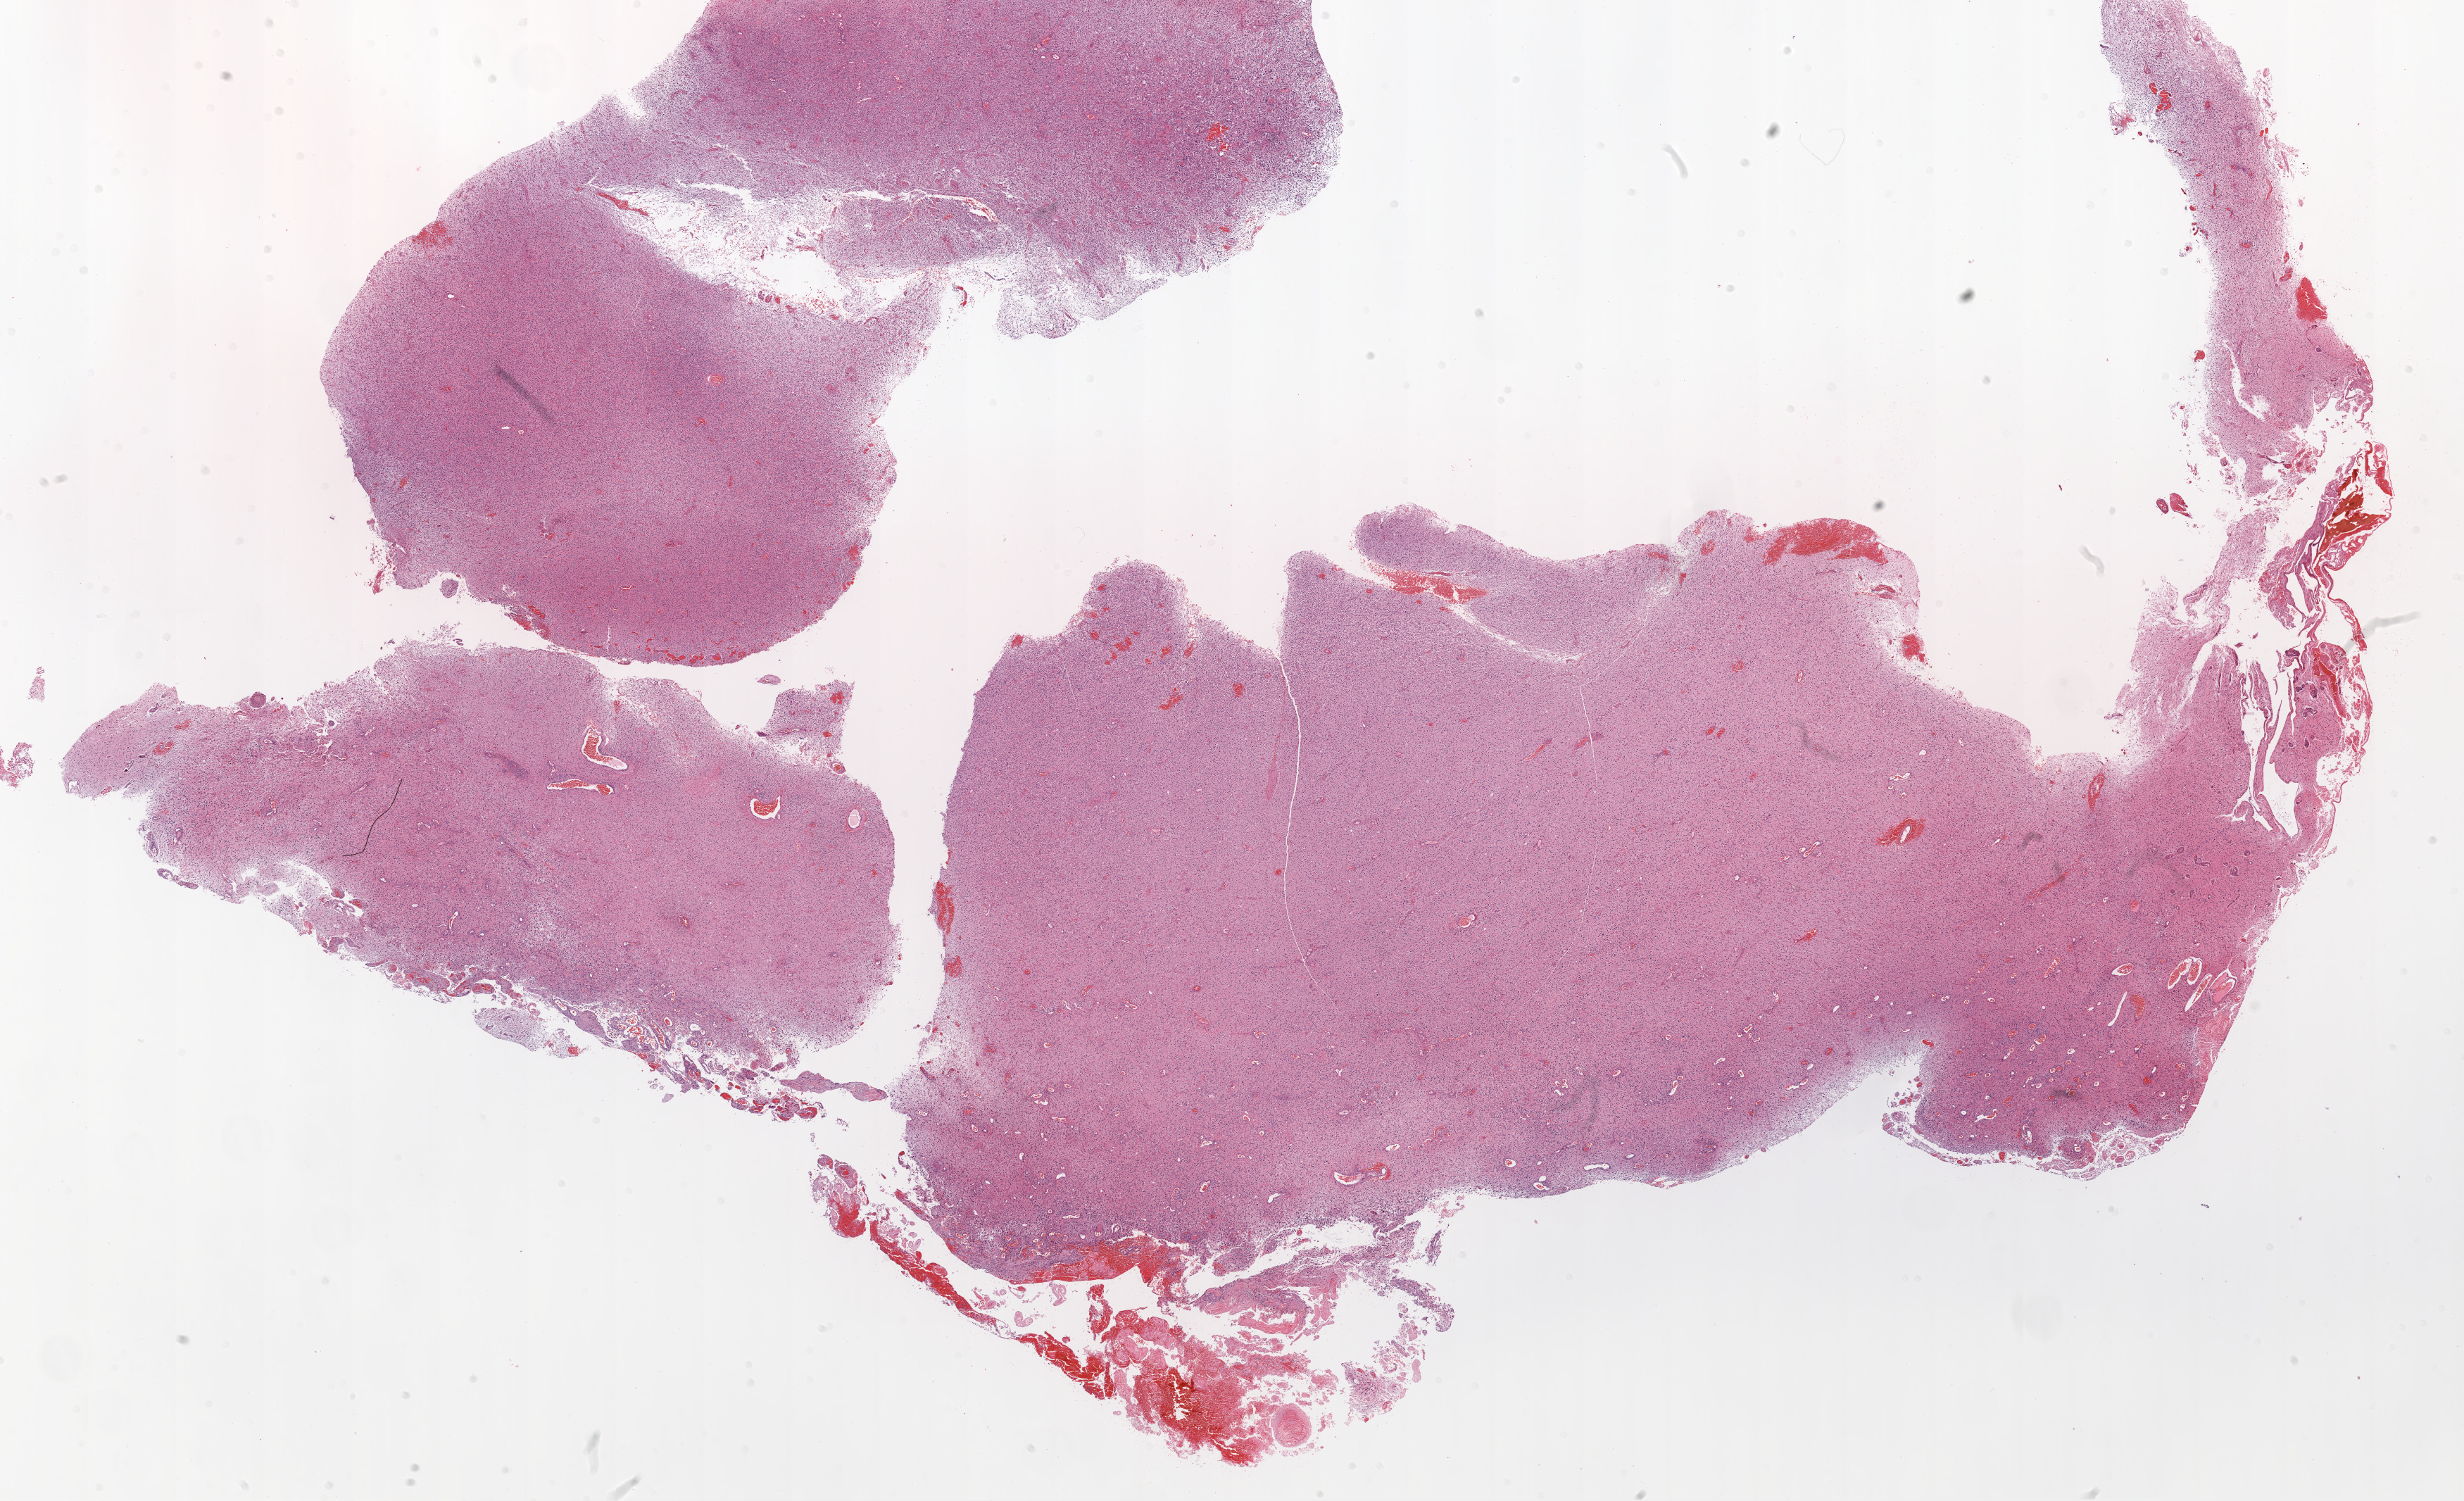
Digitized H&E-stained tissue section (whole slide) — whole scanned area (about 28.1 x 17.1 mm, slide scanned at 20x) shown as a low-resolution overview. Formalin-fixed paraffin-embedded (FFPE) diagnostic section. Brain, primary tumour sample. Male, age 38 years at initial diagnosis.
Histologic diagnosis: Glioblastoma.